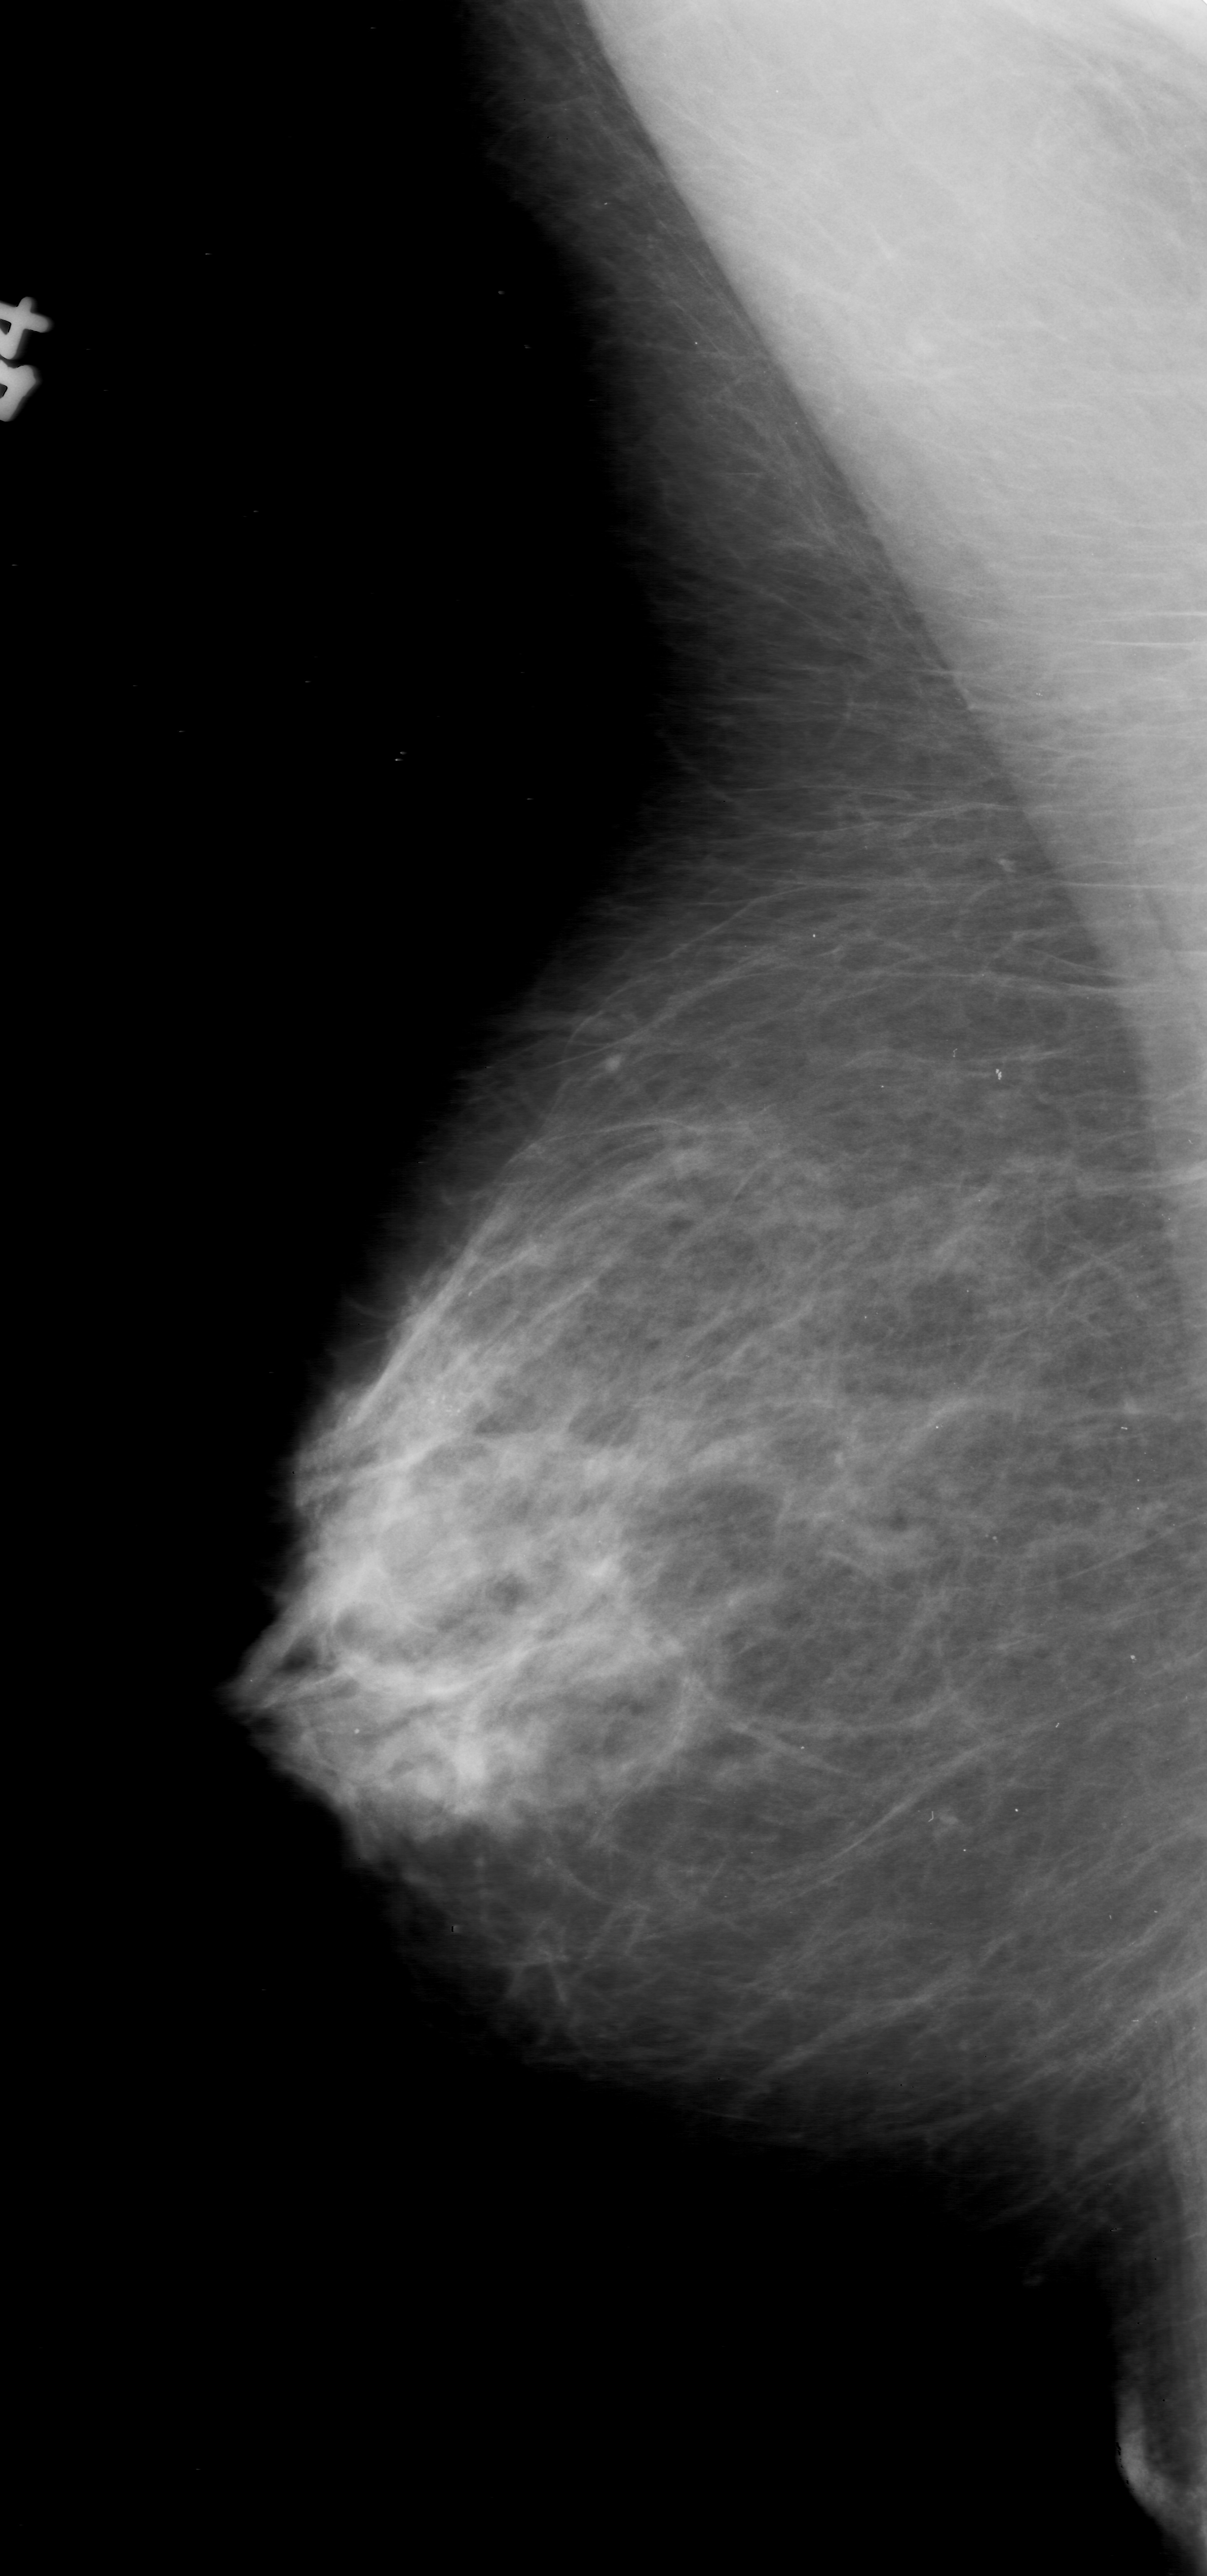
Scanned film-screen mammogram, right breast, mediolateral oblique (MLO) view, breast composition: scattered fibroglandular densities (BI-RADS density category 2 of 4).
Marked abnormality: calcifications, morphology pleomorphic, distribution clustered; BI-RADS assessment category 0; subtlety rating 4 on a 1 (subtle) to 5 (obvious) scale; pathology (as recorded): malignant.